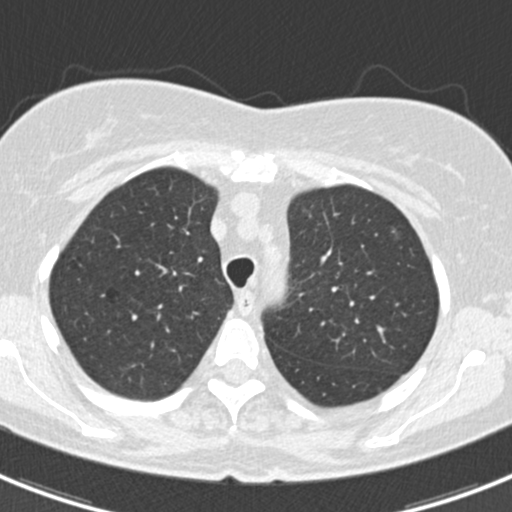
Chest CT (low-dose screening protocol), one axial image; baseline screening round; lung window (W 1500 / L -600 HU); 2 mm slice thickness; 512 × 512 image matrix, field of view 298 × 298 mm. Female, age 60 years at enrolment. Current smoker at enrolment.
Expert reader's lesion annotation, bounding box [x1, y1, x2, y2] px = [375, 225, 419, 263]. The screening reader recorded 3 non-calcified nodules or masses ≥4 mm on this exam (lingula, left lower lobe, lingula); which of them this box marks is not recorded. Participant outcome: lung cancer diagnosed 886 days after this screen (after the third annual screen) — non-small cell carcinoma, left upper lobe, poorly differentiated (G3), stage IB (AJCC 6th edition), 7 mm at pathology.